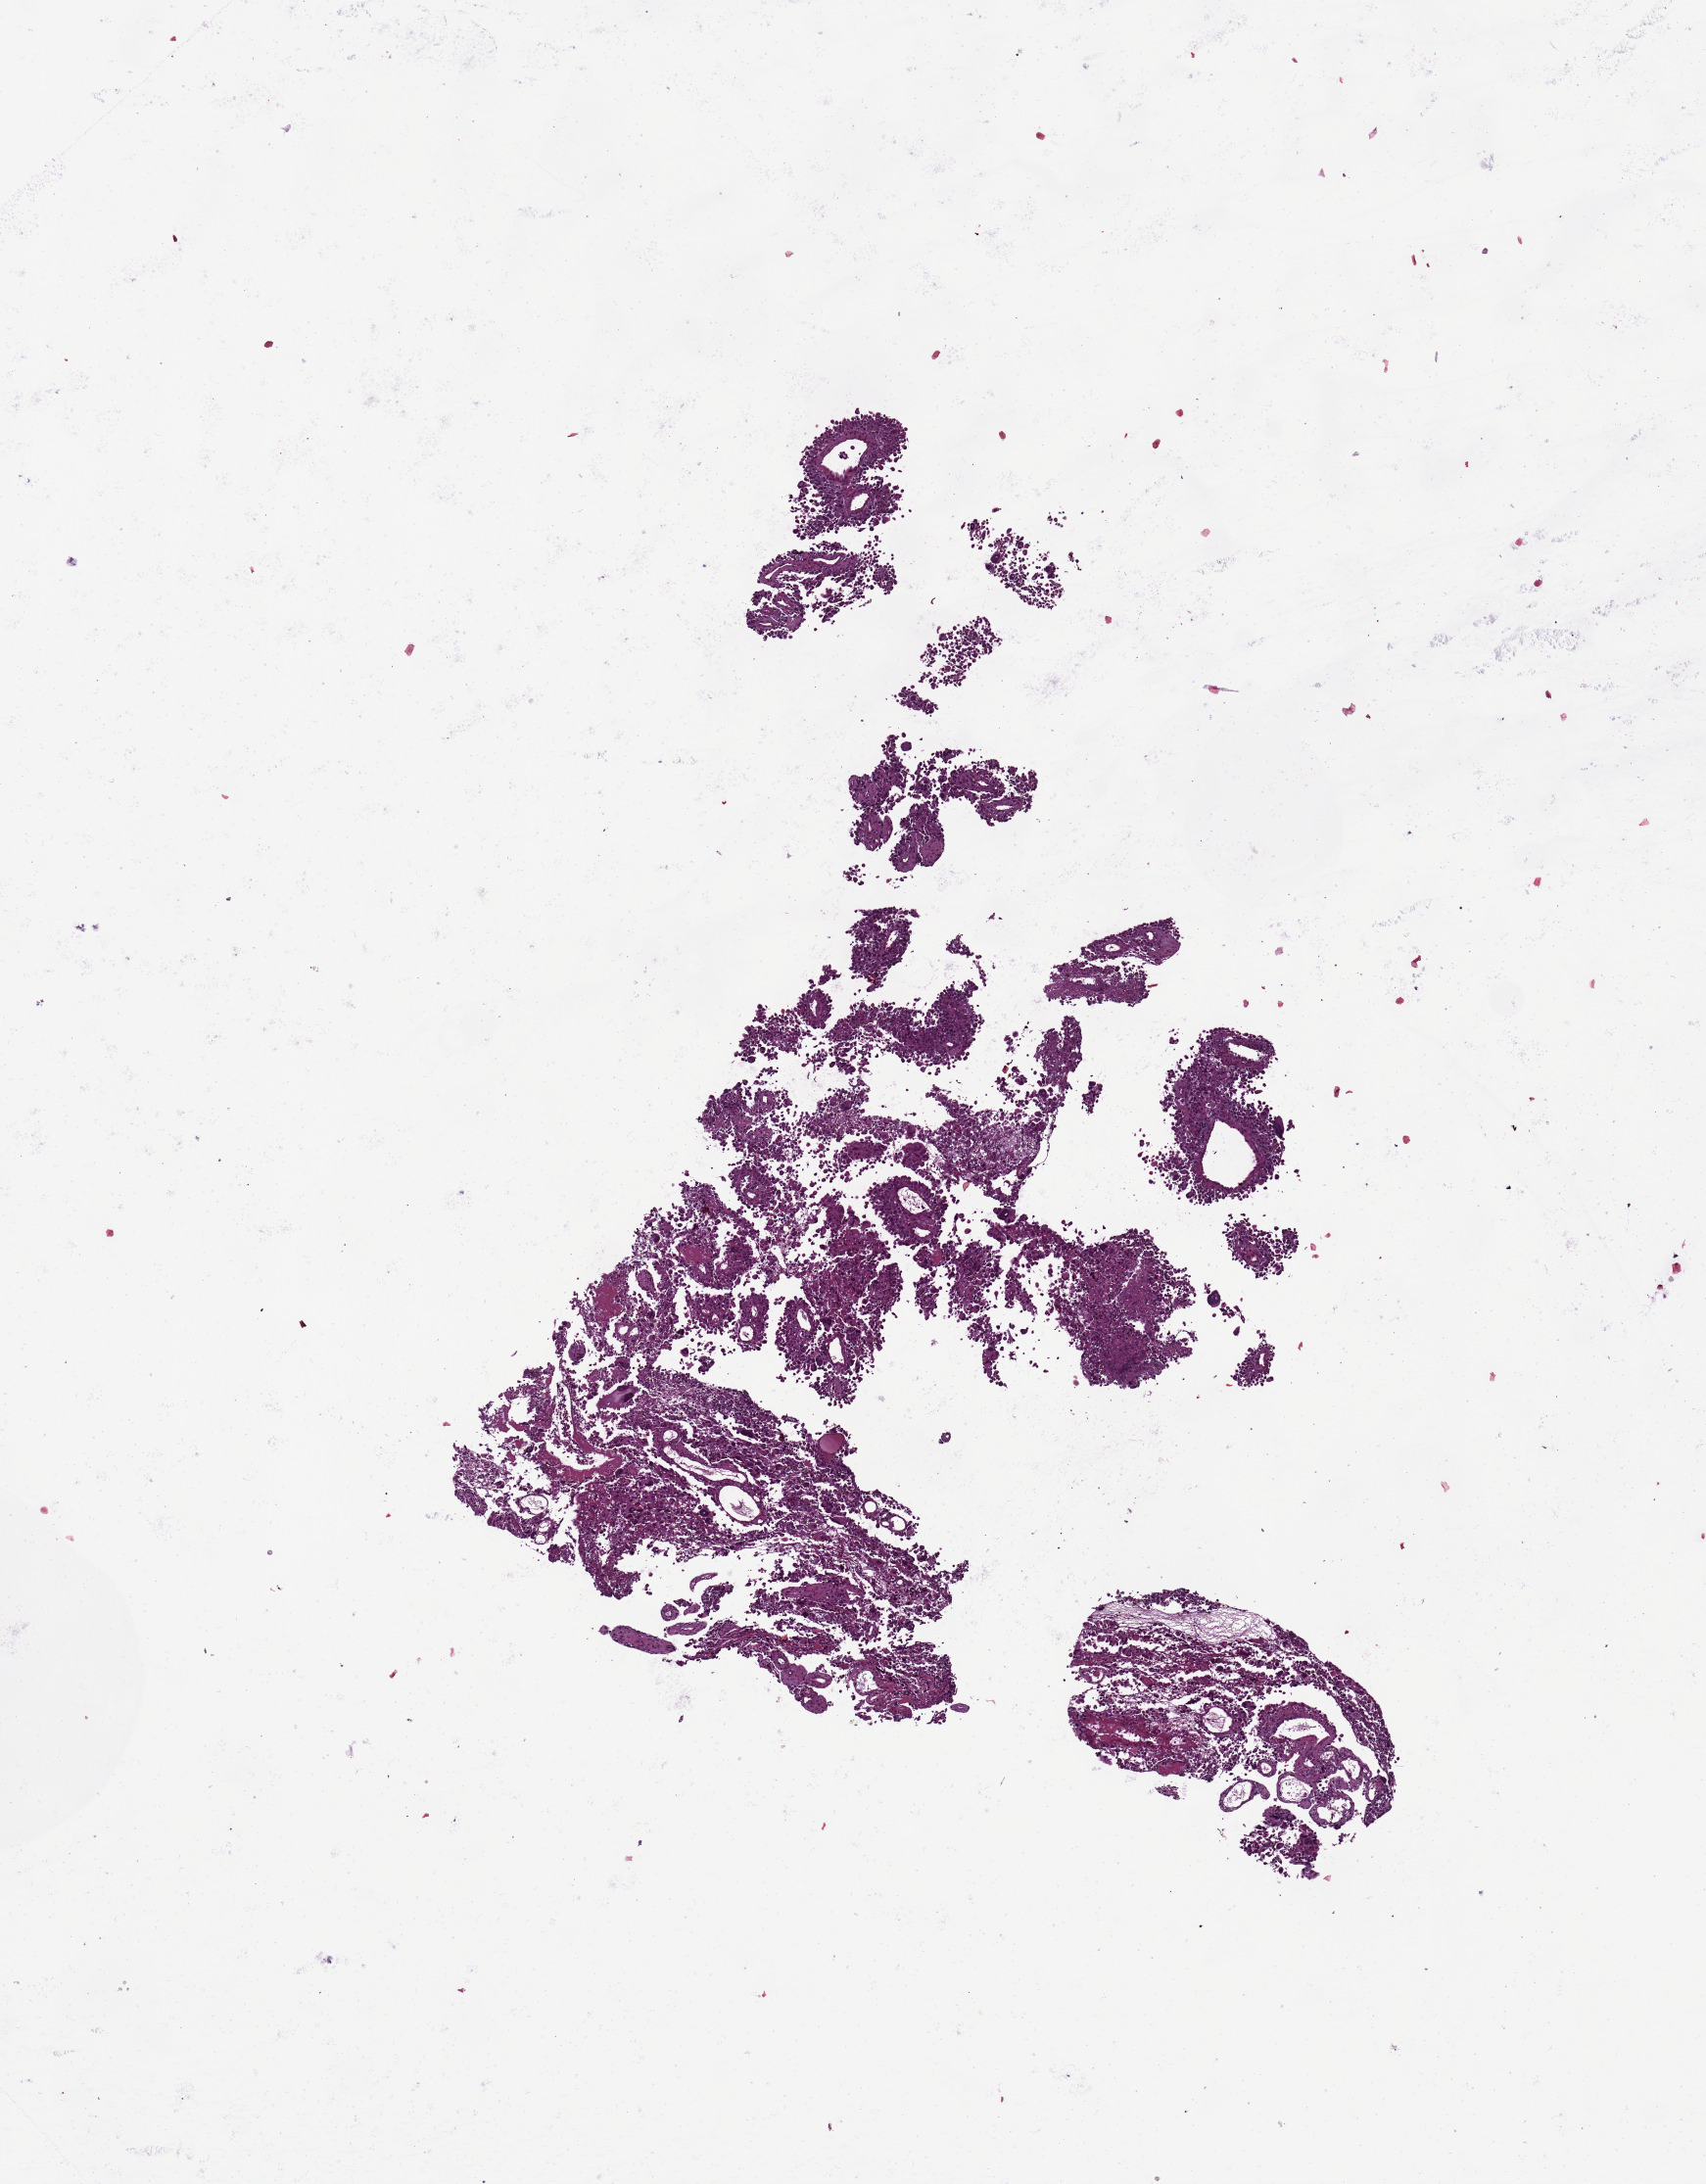
Whole-slide histology image, Hematoxylin and eosin (H&E) stained — a low-resolution overview of the entire scanned area, about 6.9 x 8.8 mm; brain, tumour tissue. 47-year-old male patient.
Histologic diagnosis: Glioblastoma.